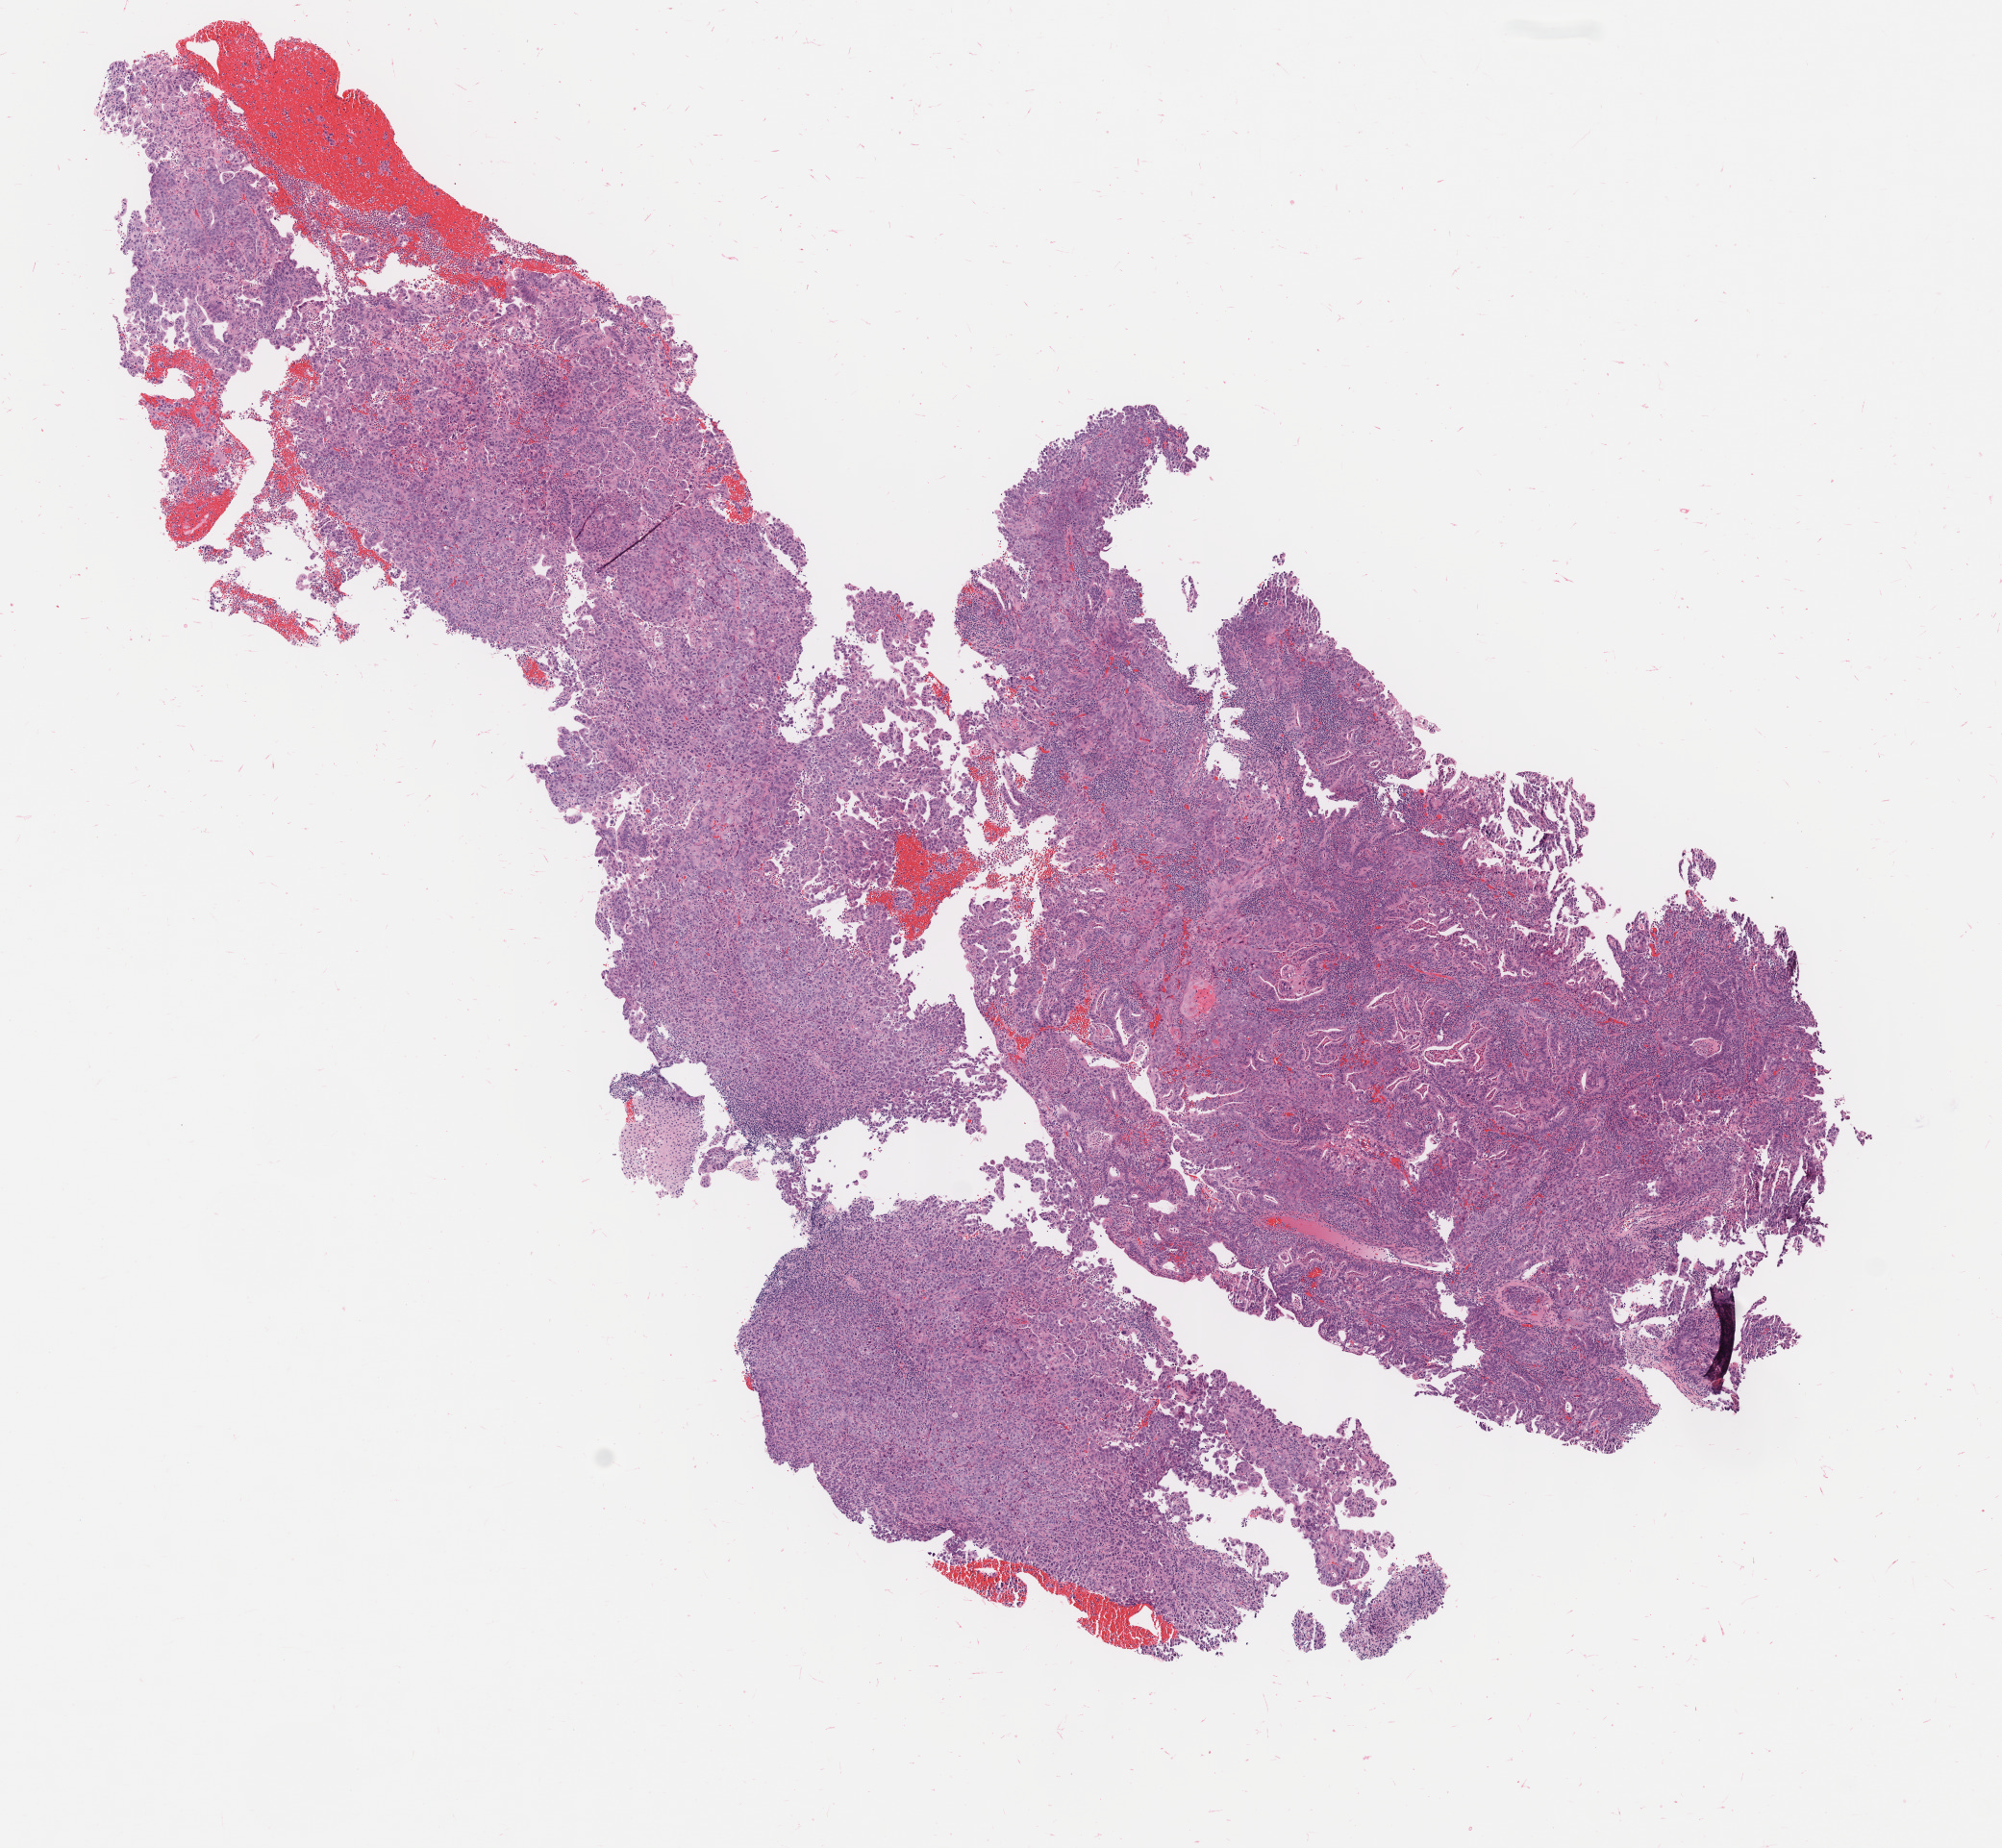
Digitized H&E-stained section — a low-resolution overview of the entire scanned area, about 8.3 x 7.6 mm, tumor tissue, site: cervix. Patient female; 57 years old.
• histologic diagnosis: Adenocarcinoma, NOS